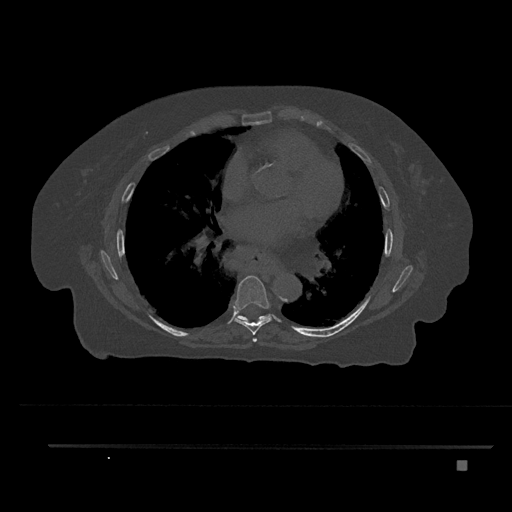
CT including the spine, one axial slice. Slice 476 of 797 in the series (ordered by position). Reconstruction kernel Br40s/3. Bone window (W 1800 / L 400 HU). 512 × 512 image matrix, field of view 437 × 437 mm. Patient: female, 76 years. From the clinical record (not read from this slice): primary cancer: lung; vertebrae with lytic lesions (as recorded): T11, L3.
Structures marked on this image (semi-automatic segmentation, software-assisted and operator-edited):
- T6 vertebra: box from (x=252, y=338) to (x=257, y=342) px
- T7 vertebra: (x=233, y=275)–(x=272, y=335)
- T8 vertebra: (x=236, y=314)–(x=271, y=322)